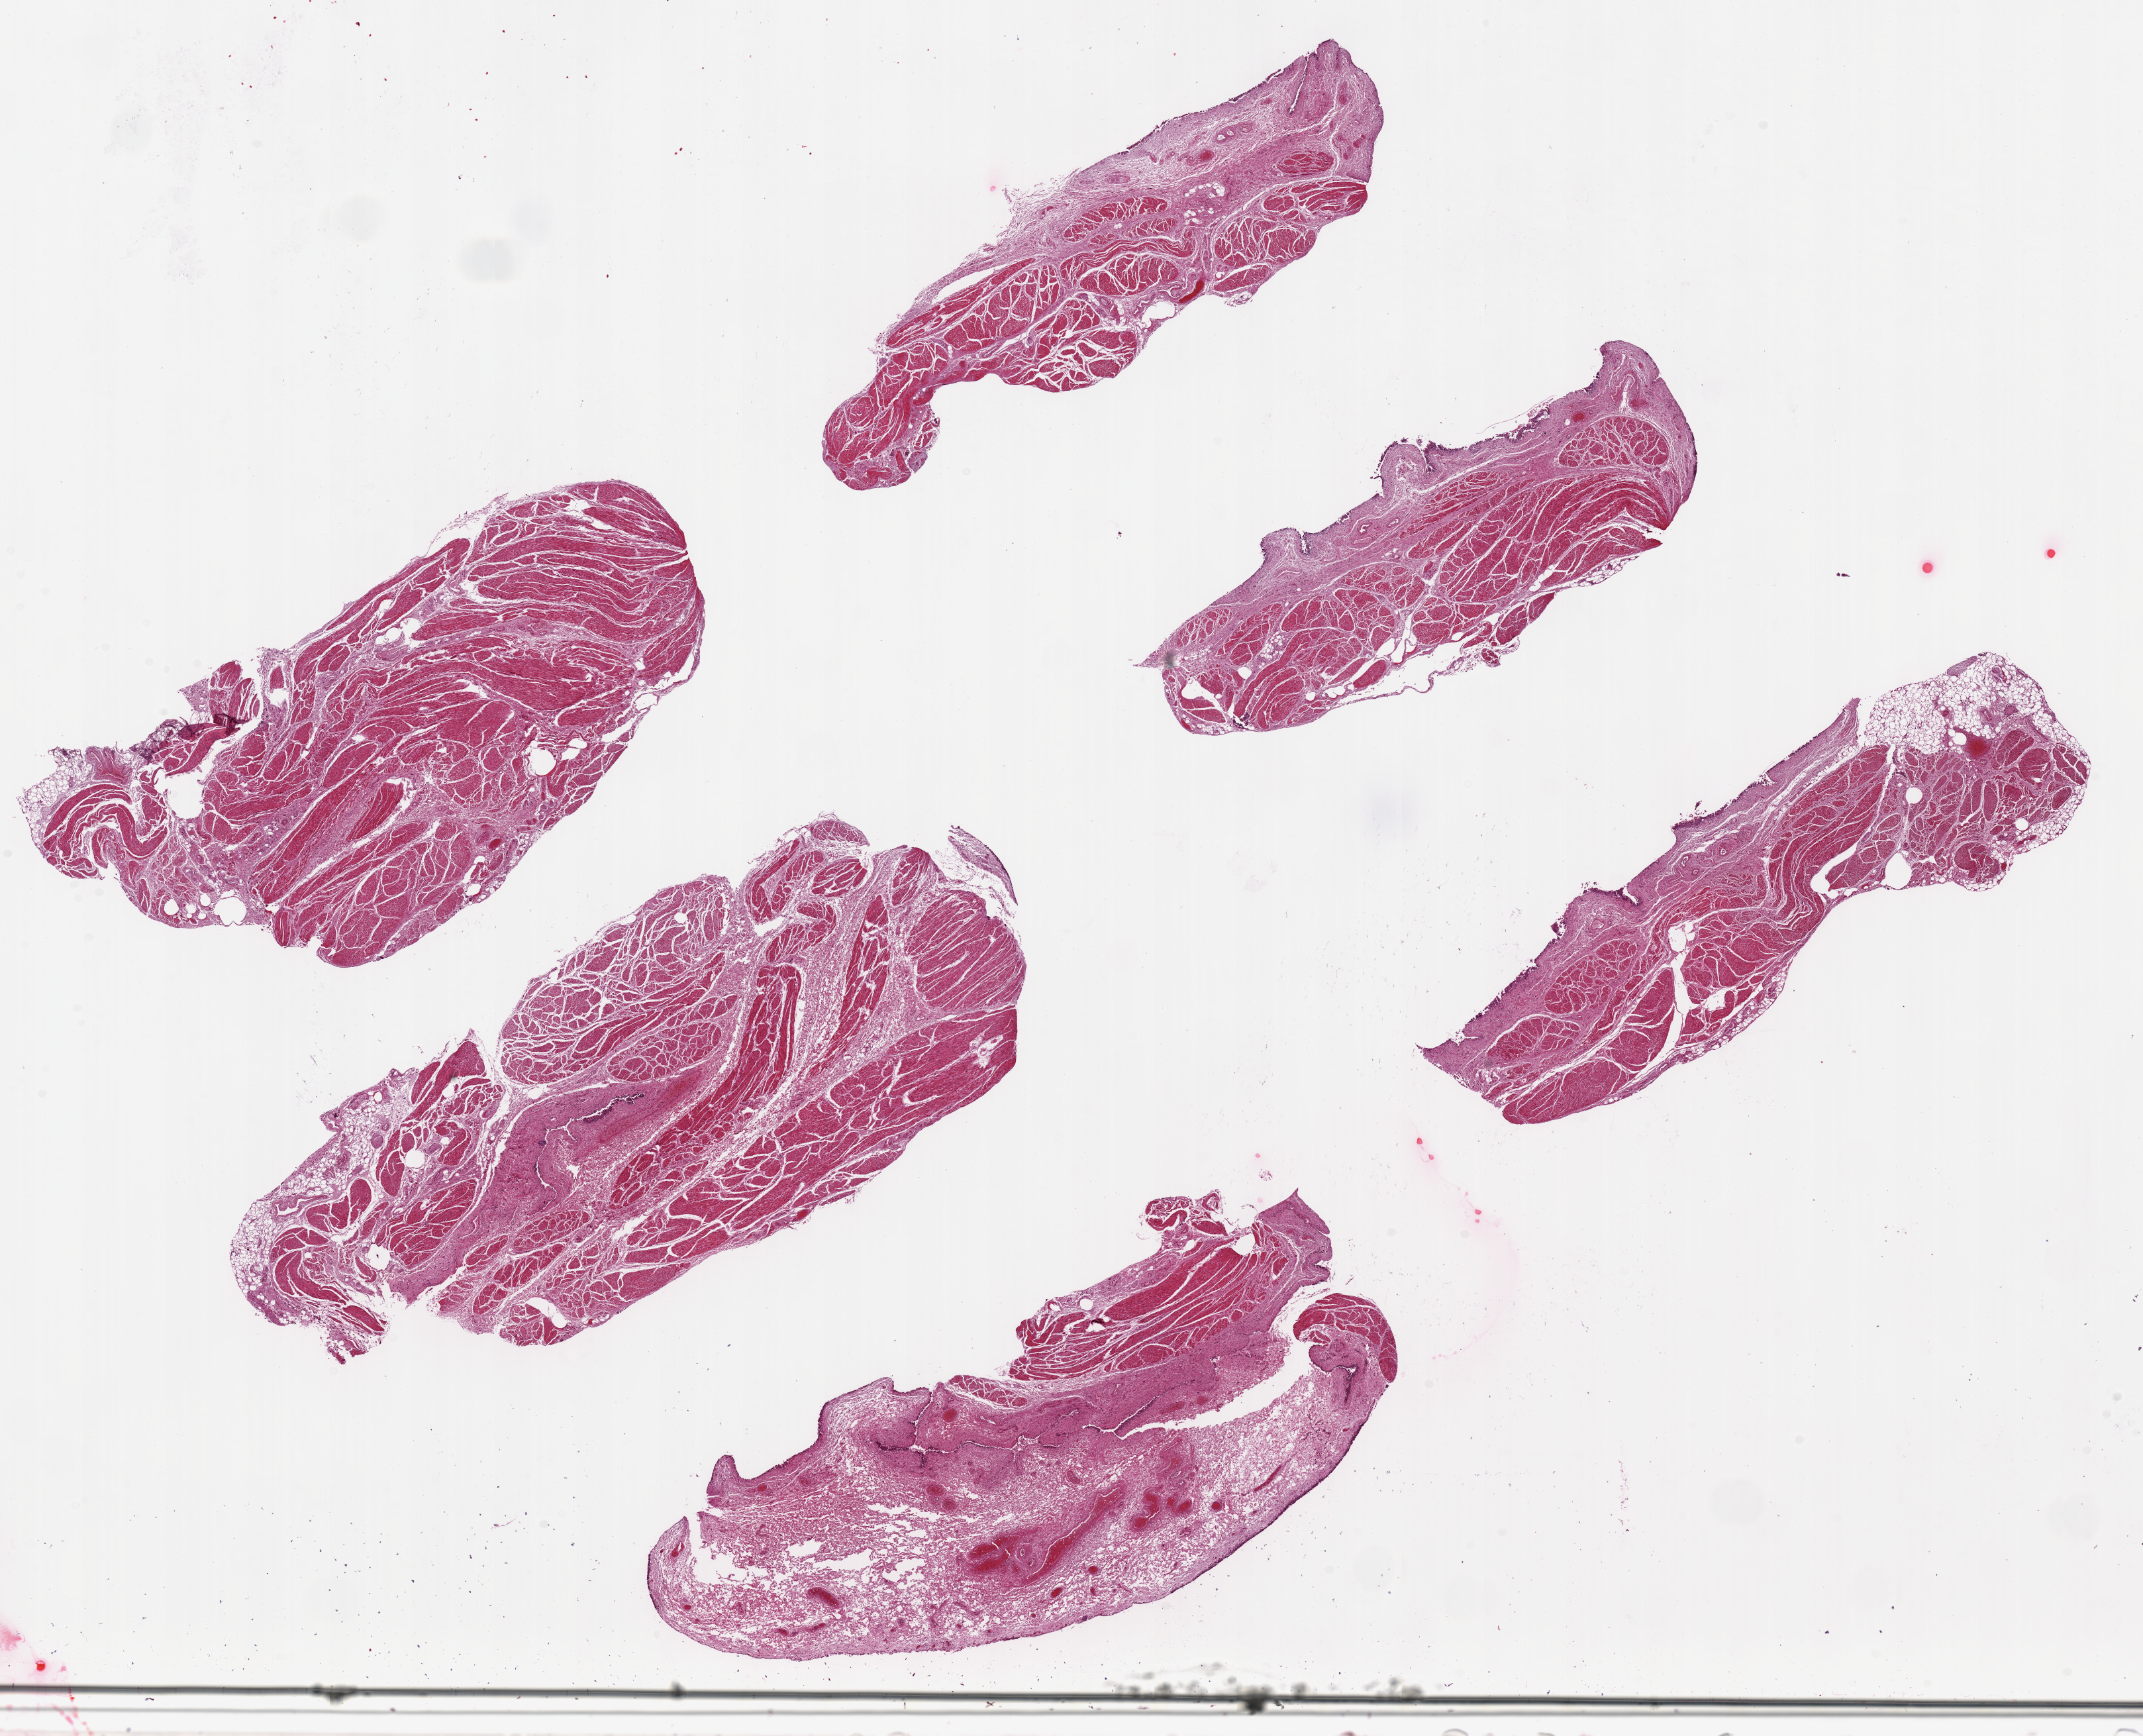
Digitized hematoxylin and eosin (H&E)-stained section — a low-resolution overview of the entire scanned area, about 25.6 x 20.7 mm, PAXgene-fixed paraffin-embedded (PFPE) section, section of urinary bladder (target tissue), donor tissue sample. Female donor.
• review note (as recorded): 8 ~7.5x2.5mm pieces. Urothelium completely sloughed